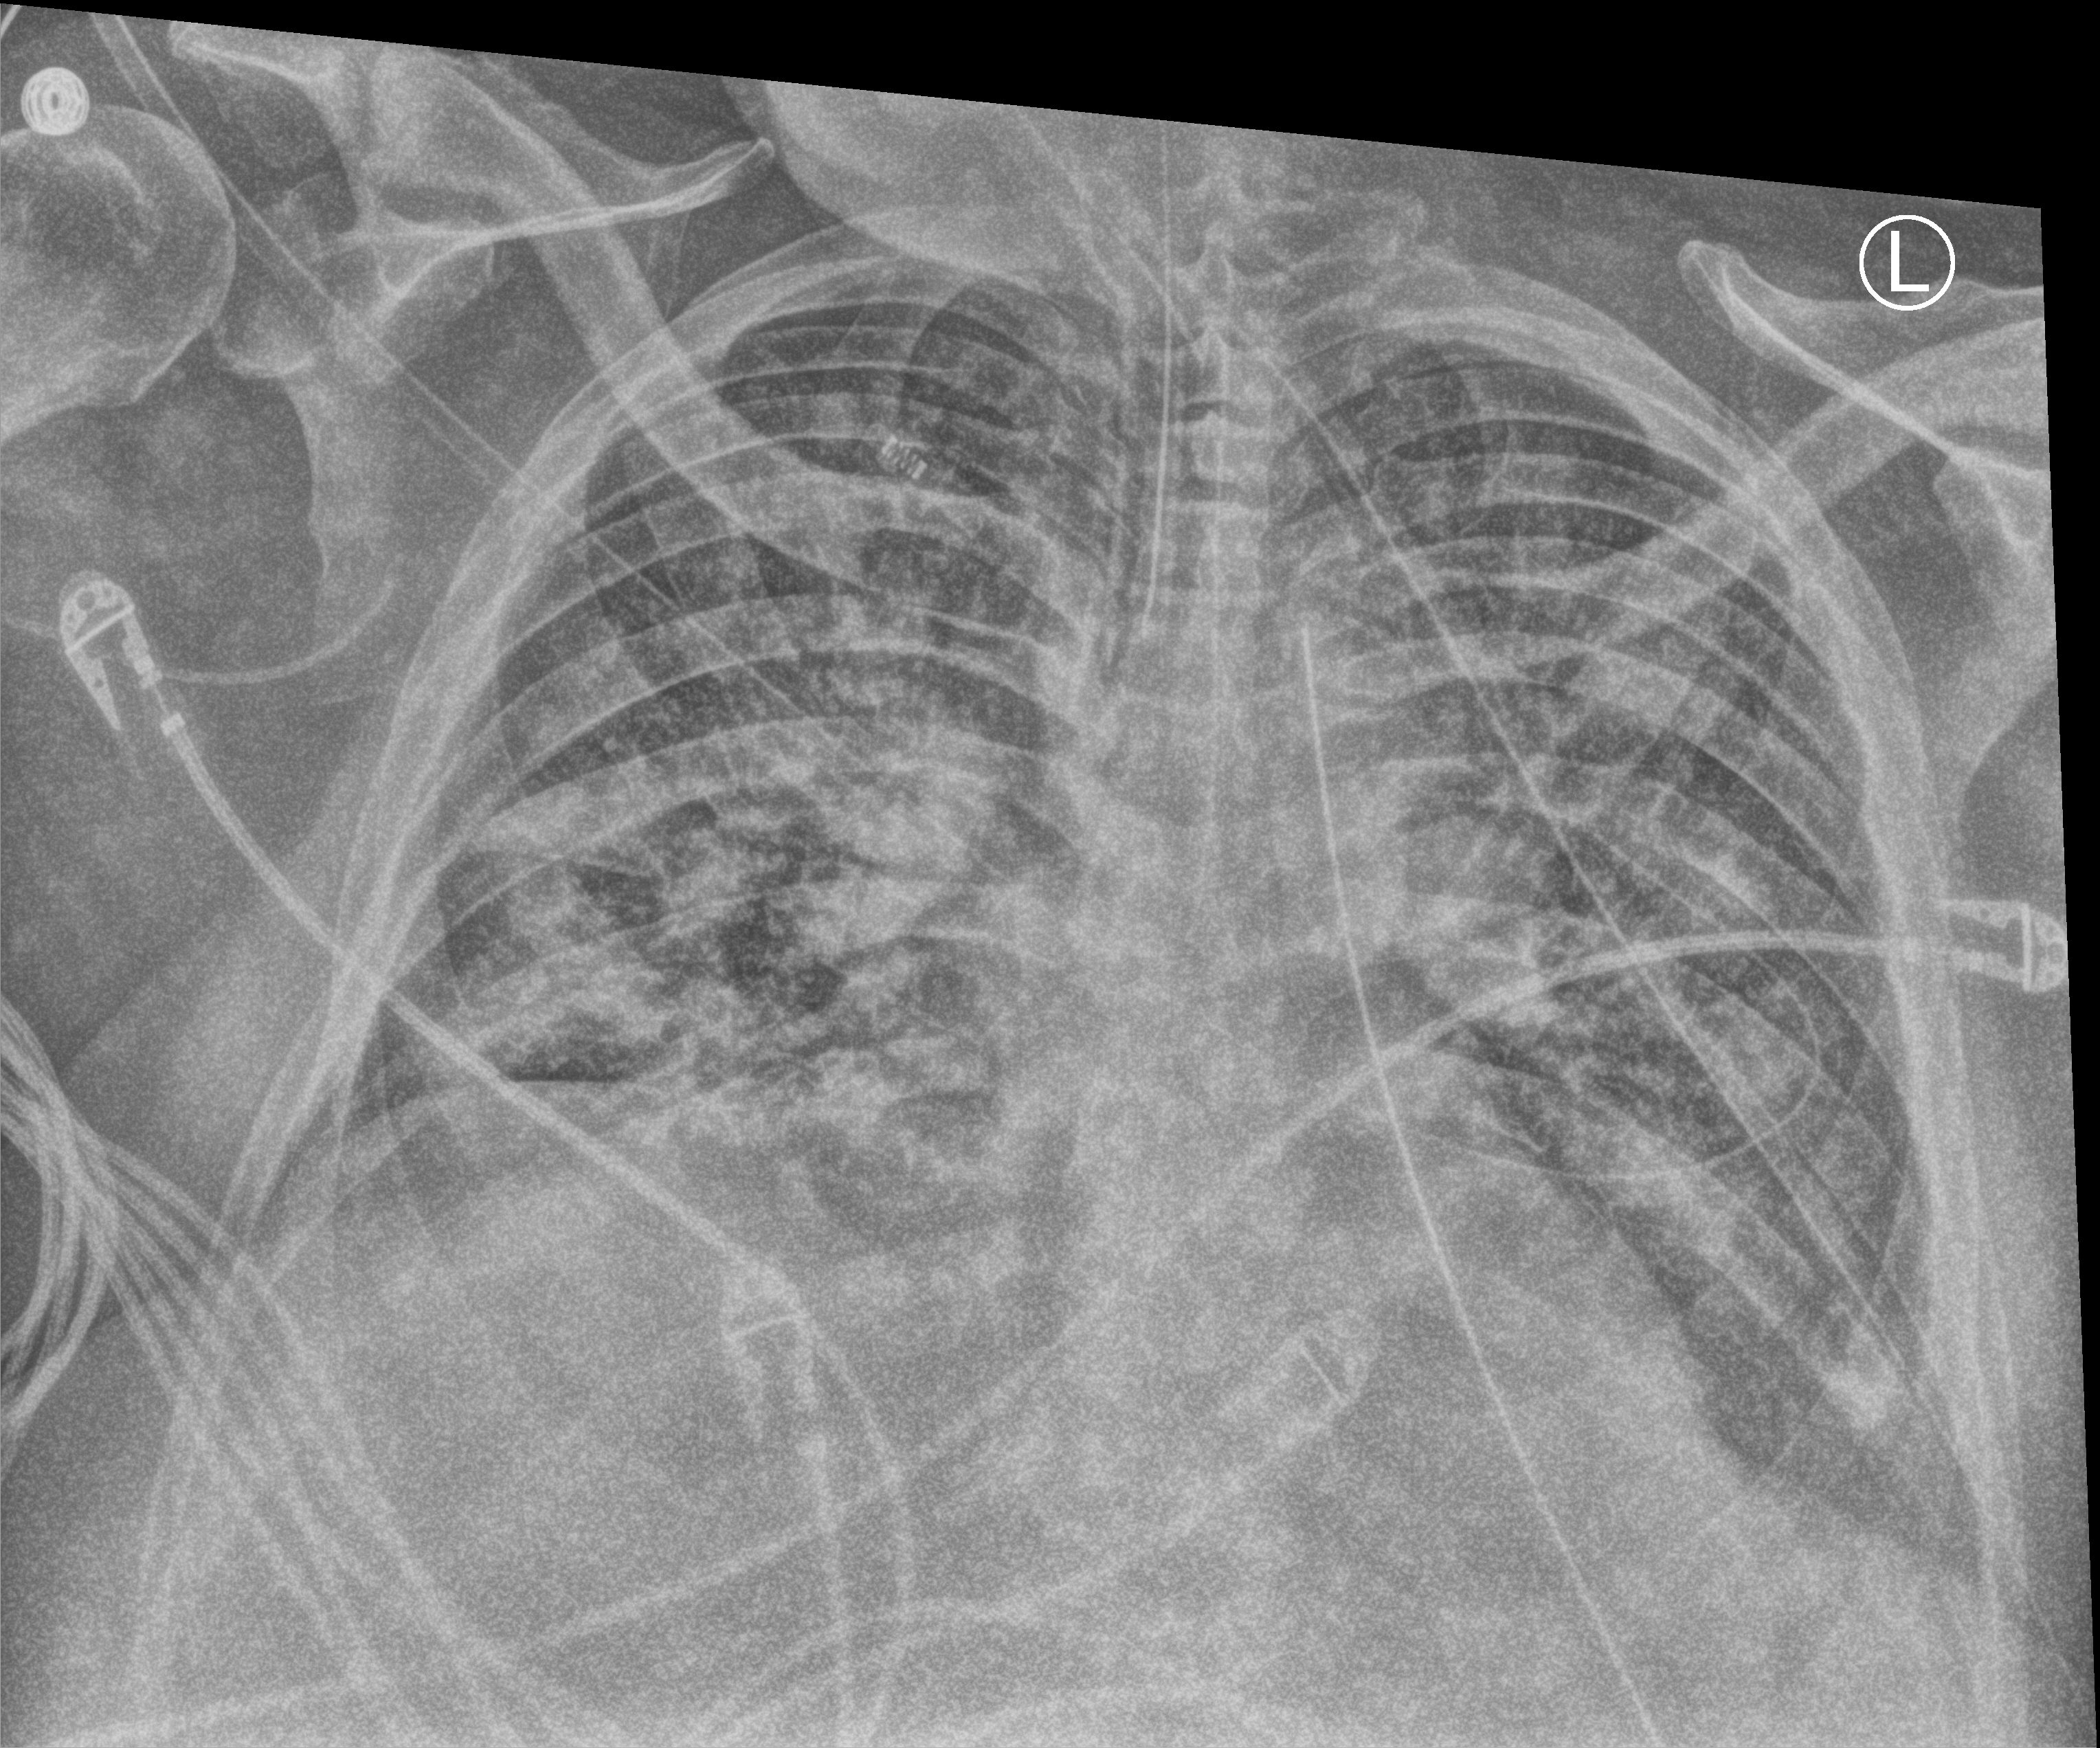
Chest X-ray (portable). Male patient hospitalised with COVID-19, age 60–74 years.
Hospital-stay facts (about this admission, not read from this image; timing relative to this image not recorded): length of hospital stay: 34 days; chronic kidney disease (admission record): no.